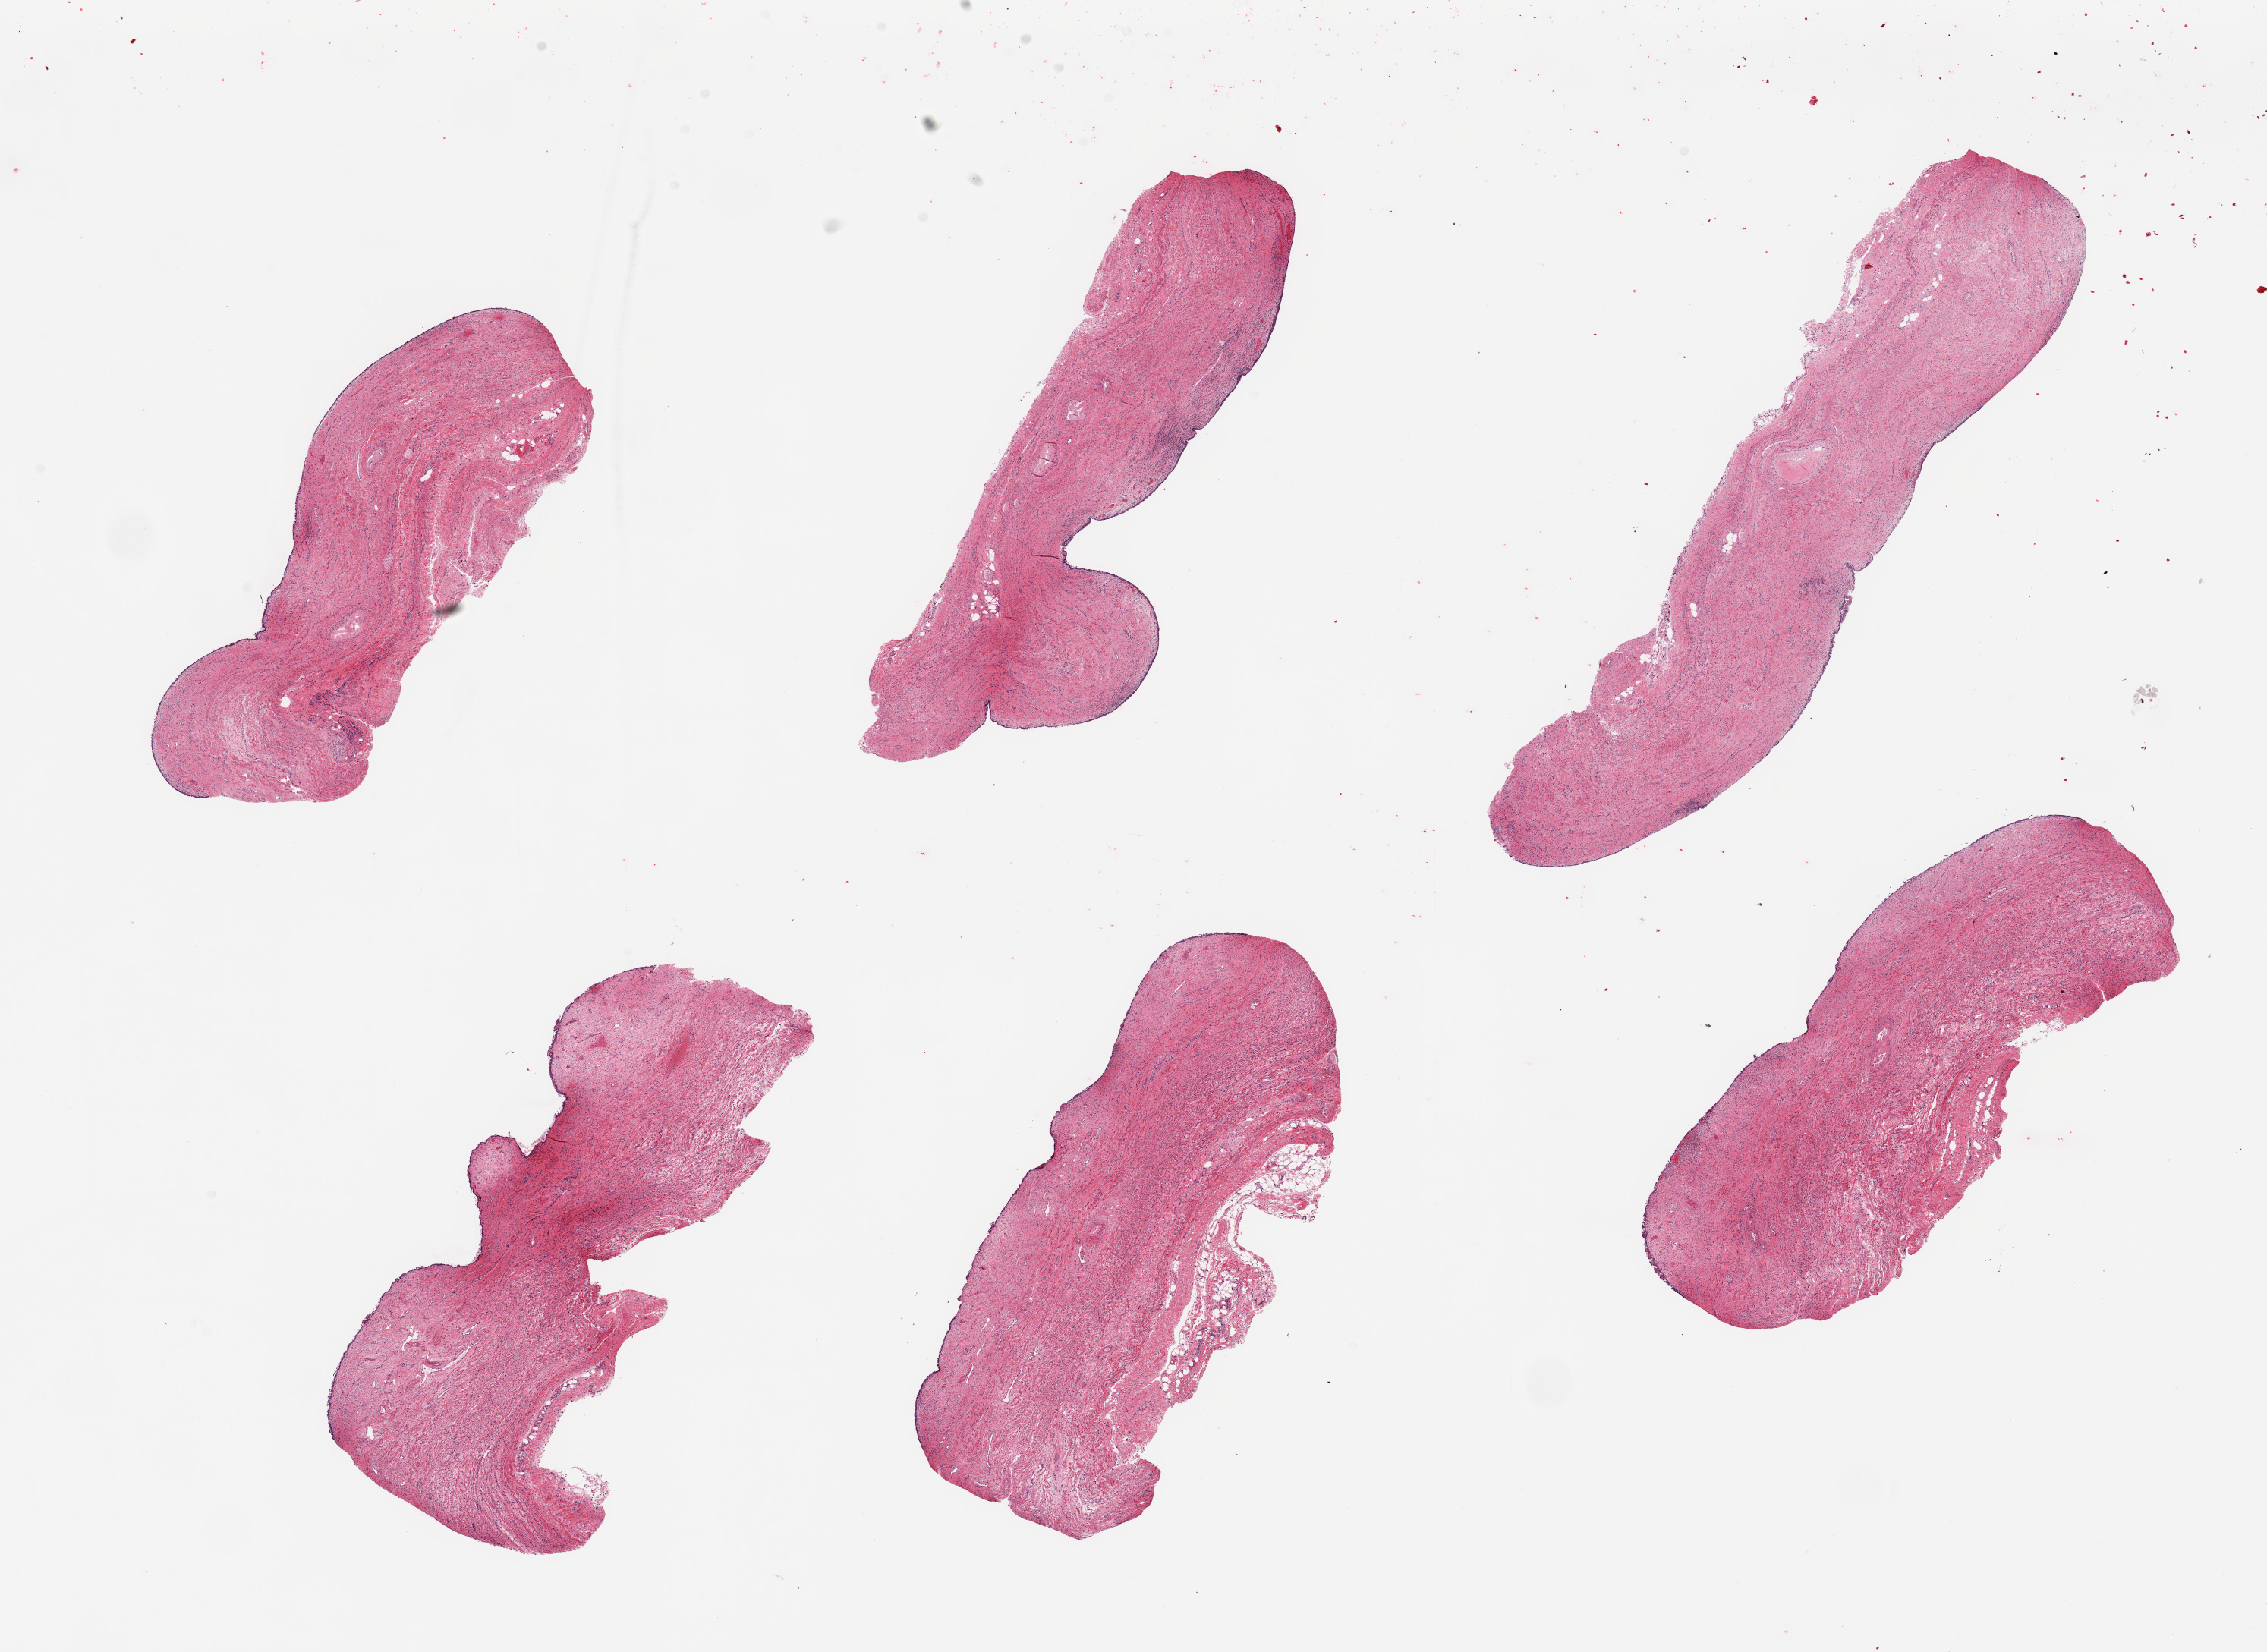
Whole-slide image, H&E stain, whole scanned area (about 23.6 x 17.2 mm) shown as a low-resolution overview; PAXgene-fixed, paraffin-embedded tissue; sampled site (target tissue): vagina; donor tissue sample. Donor sex: female.
* pathologist's review note for this sample: 6 pieces; largely sloughed, atrophic squamous epithelium